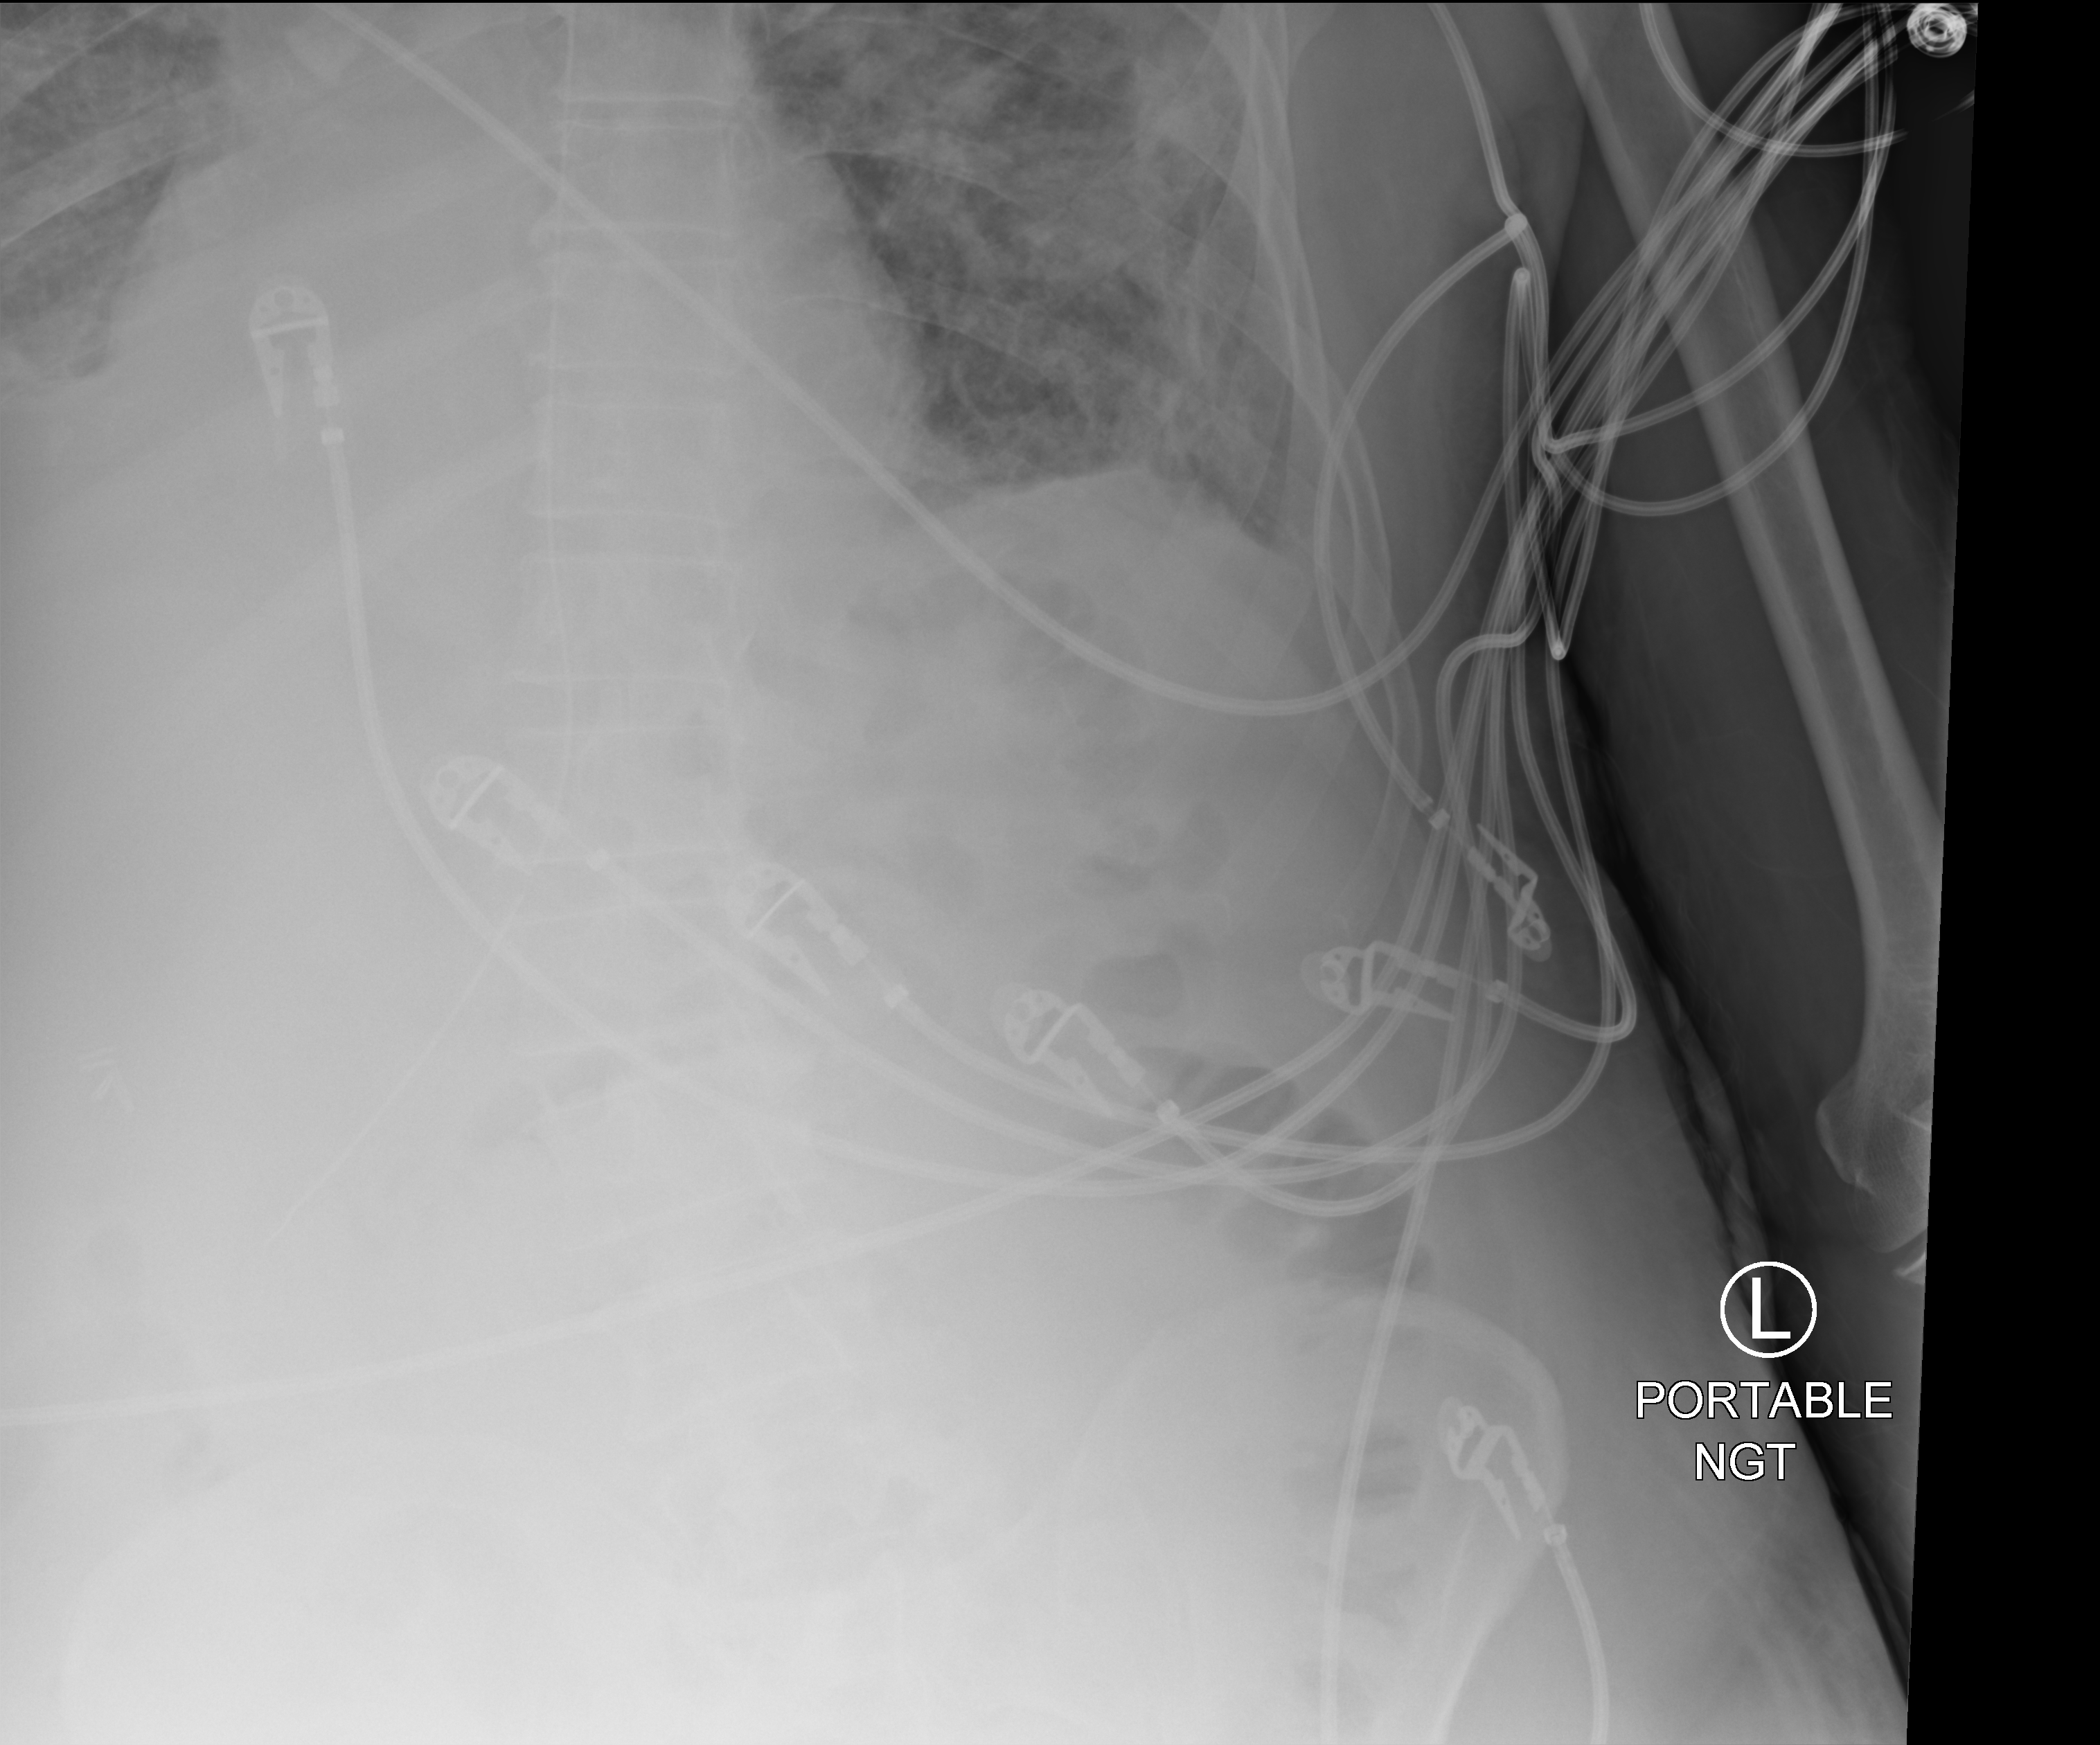
Chest X-ray (portable), anteroposterior (AP) projection. Patient hospitalised with COVID-19; male, aged 75–90 years.
Hospital-stay facts (about this admission, not read from this image; timing relative to this image not recorded): mechanically ventilated during this hospital stay: yes.